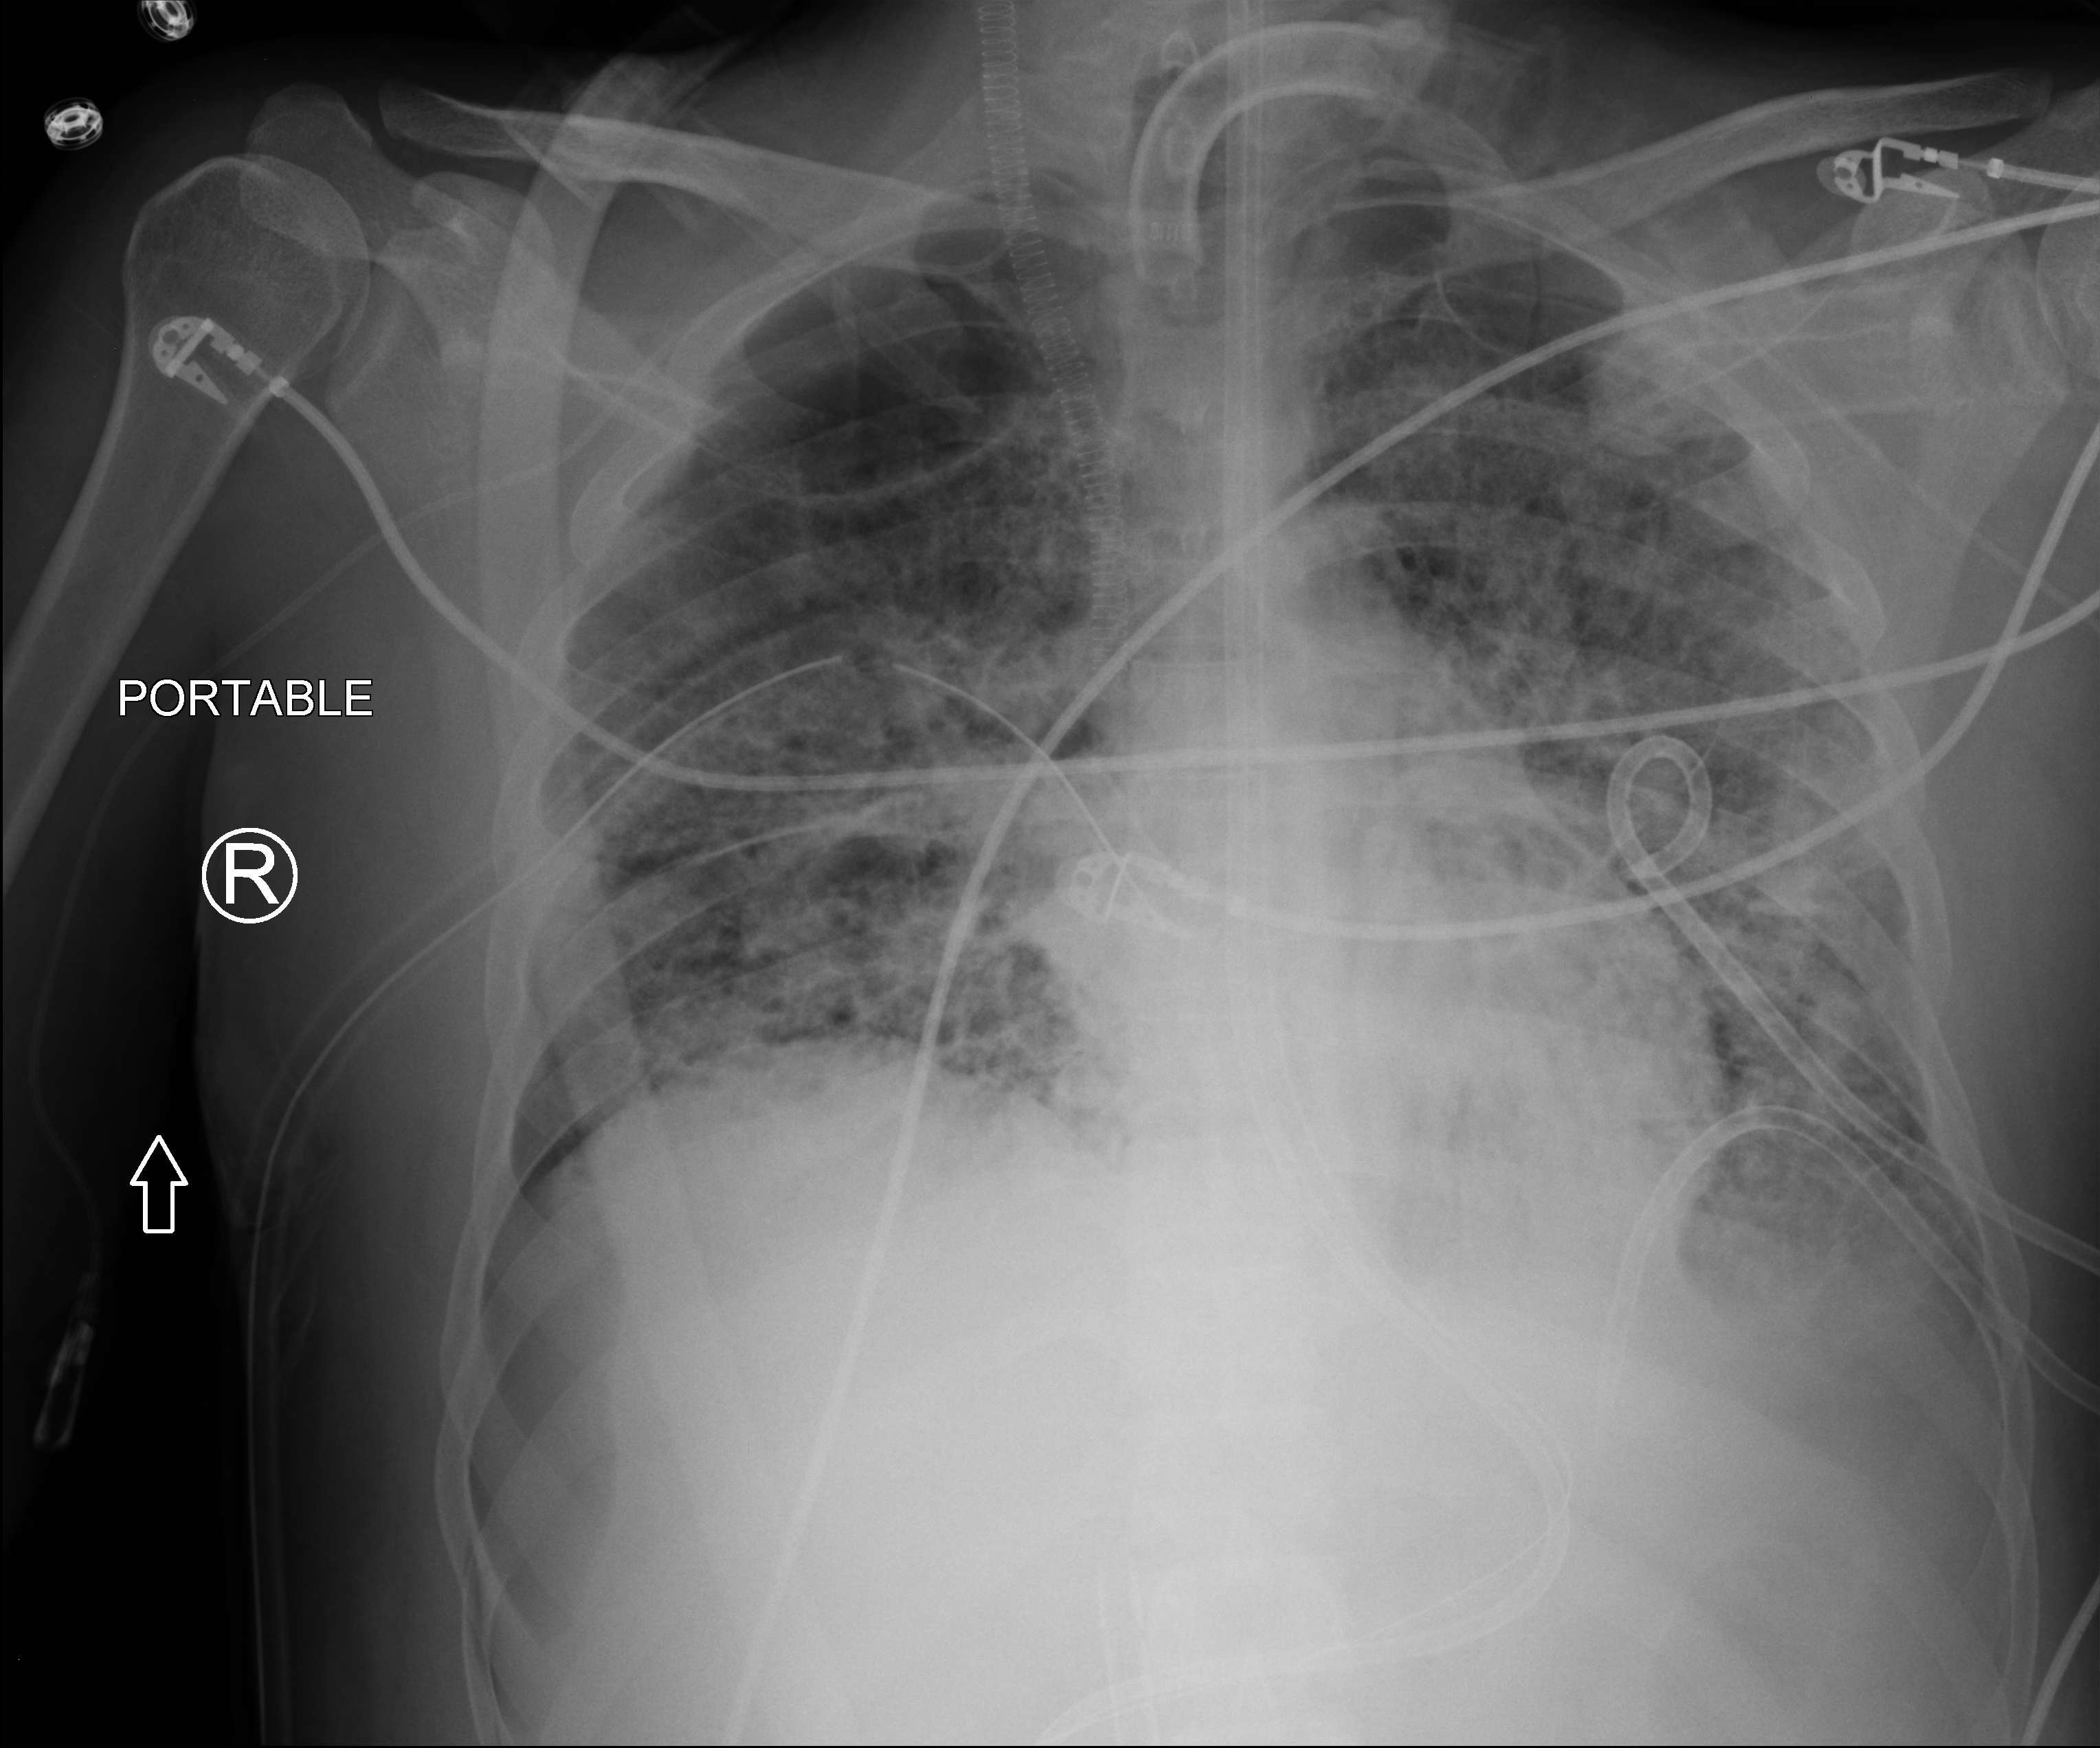
Portable chest radiograph, anteroposterior (AP) projection. Patient hospitalised with COVID-19, aged 18–59 years.
From the hospital-stay record, not from the radiograph (when in the stay this image was taken is not recorded):
- mechanically ventilated during this hospital stay: yes
- diabetes (admission record): no